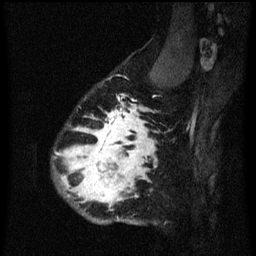
Breast MRI (dynamic contrast-enhanced), one sagittal slice; position 50 of 60 along the scan axis; dynamic contrast-enhanced series, image 2 of 3 at this slice position (ordered by acquisition); 1.5 T; TE 4.2 ms, TR 8.4 ms; 2 mm slice thickness; 256 × 256 image matrix, field of view 180 × 180 mm. Patient: female, 34 years. From the clinical record (not read from this slice): setting: breast cancer imaged before/during neoadjuvant chemotherapy; receptor status: HR-positive, HER2-negative.
Structures marked on this image (semi-automatically segmented with operator editing):
- analysis volume of interest (the breast-tissue region the enhancement analysis was run in; not a lesion): bounding box [x1, y1, x2, y2] px = [54, 58, 173, 225]
- tumour enhancement mask (voxels above the 70 % enhancement threshold inside the analysis volume of interest): [58, 104, 155, 205]